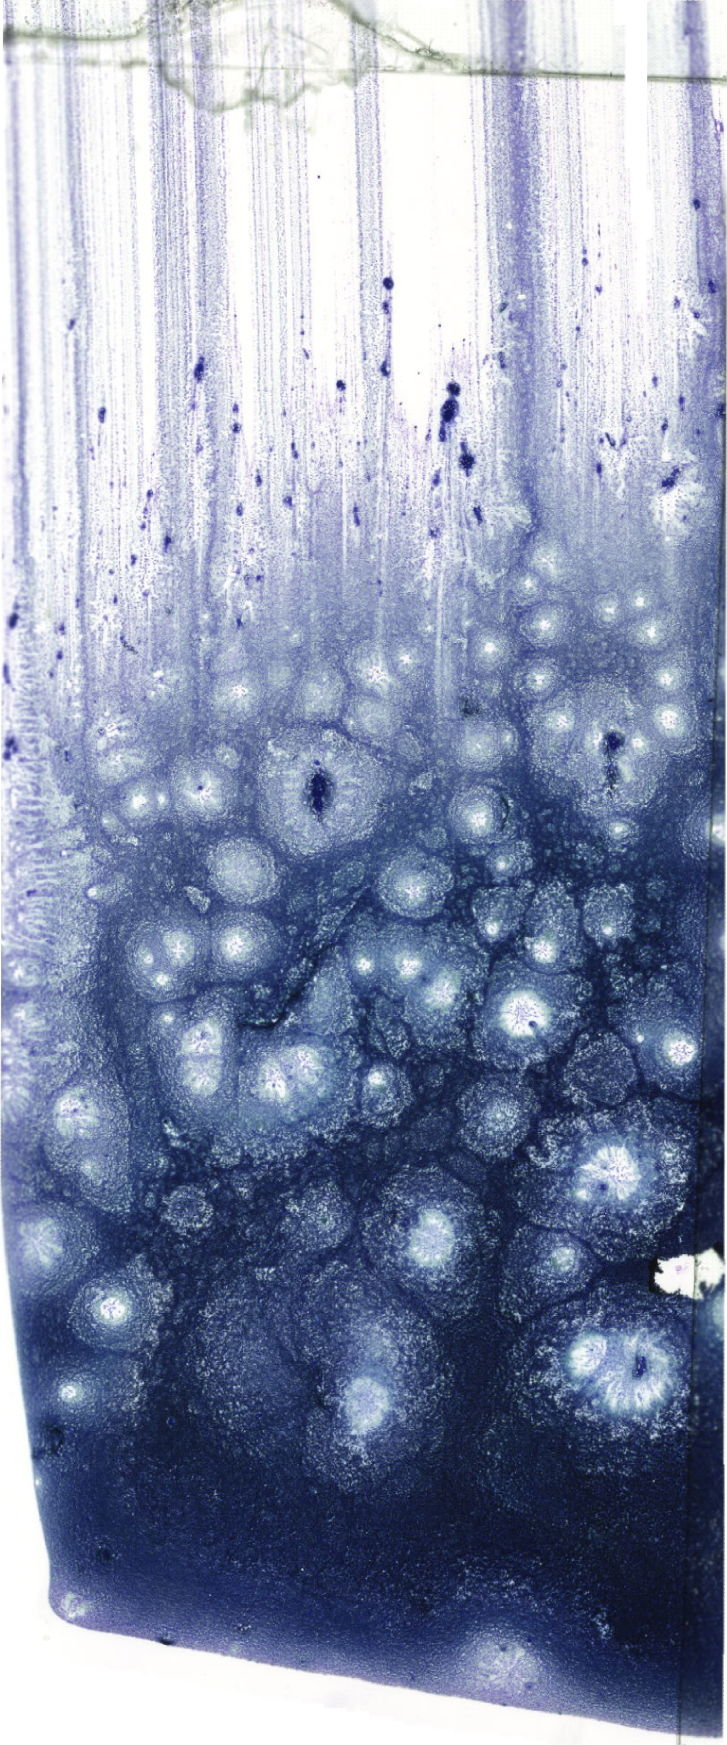
May-Grünwald–Giemsa-stained marrow aspirate smear (whole slide), a low-resolution overview of the entire scanned area, about 20.6 x 49.5 mm. Male patient.
Diagnosis: Acute Myeloid Leukemia with Maturation.